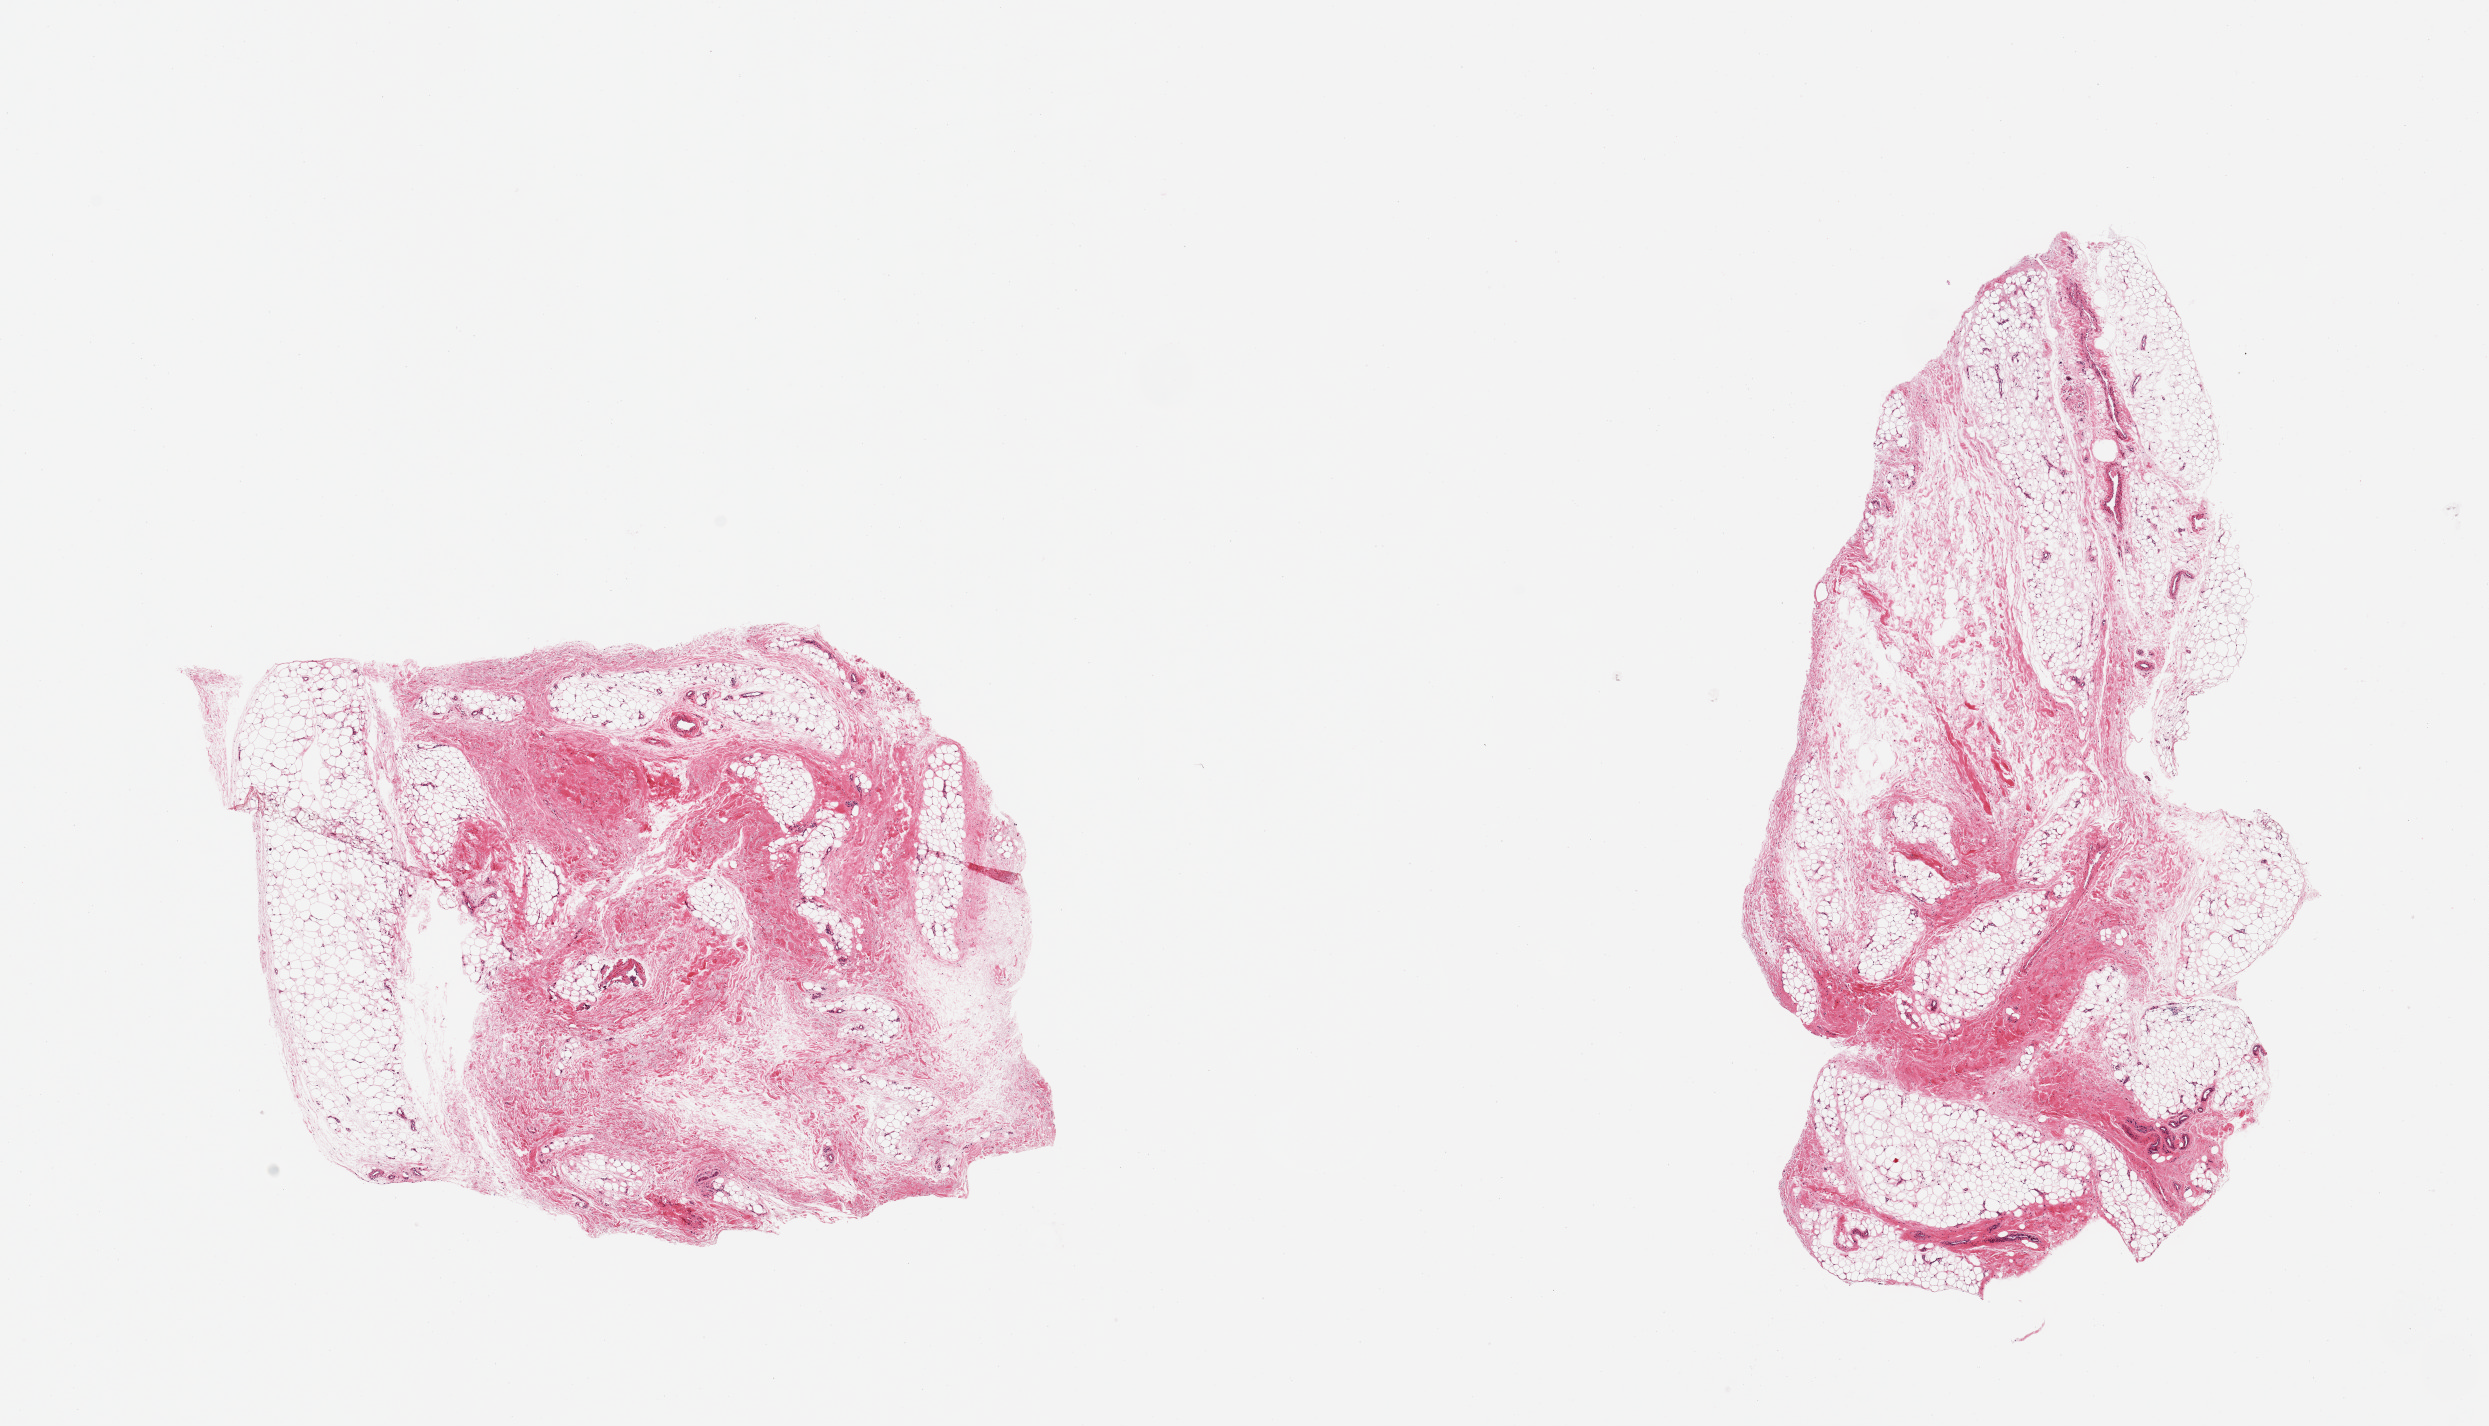
Whole-slide image, hematoxylin and eosin (H&E) stain, brightfield, a low-resolution overview of the entire scanned area, about 19.7 x 11.3 mm (from a 20x scan). PAXgene-fixed paraffin-embedded (PFPE) section. Sampled site (target tissue): adipose tissue. Tissue donor sample. Donor sex: male.
Review note (as recorded): 2 pieces; 30% & 40% fibrous content.